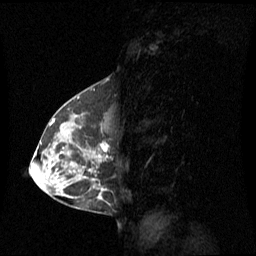
Breast MRI (dynamic contrast-enhanced), one sagittal slice; slice 32 of 60 in the series (ordered by position); dynamic contrast-enhanced series, image 2 of 3 at this slice position (ordered by acquisition); 1.5 T; TE 4.2 ms, TR 8.4 ms; 2 mm slice thickness; 256 × 256 image matrix, field of view 270 × 270 mm. Patient: female, 42 years. Case-level facts recorded for this patient, not image findings: setting: breast cancer imaged before/during neoadjuvant chemotherapy; receptor status: HR-positive, HER2-negative.
Structures marked on this image (semi-automatically segmented with operator editing):
- analysis volume of interest (the breast-tissue region the enhancement analysis was run in; not a lesion): bounding box <56,113,109,185> (left, top, right, bottom; pixels)
- tumour enhancement mask (voxels above the 70 % enhancement threshold inside the analysis volume of interest): <99,143,108,157>